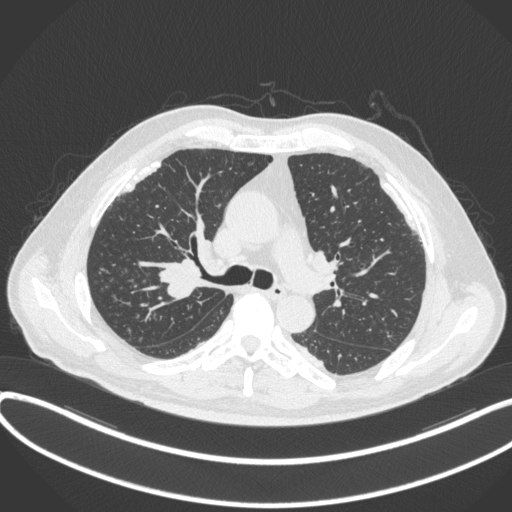
Chest CT, one axial slice; slice 275 of 455 in the series (ordered by position); 120 kVp; lung window (W 1500 / L -600 HU); 1 mm slice thickness; 512 × 512 image matrix. Patient: male, 58 years. Case-level facts recorded for this patient, not image findings: clinical TNM (as recorded): T1c N0 M0.
Outlined on this slice (bounding box drawn by a radiologist):
- lung tumour (recorded histology: squamous cell carcinoma): bounding box [x1, y1, x2, y2] px = [151, 255, 203, 308]